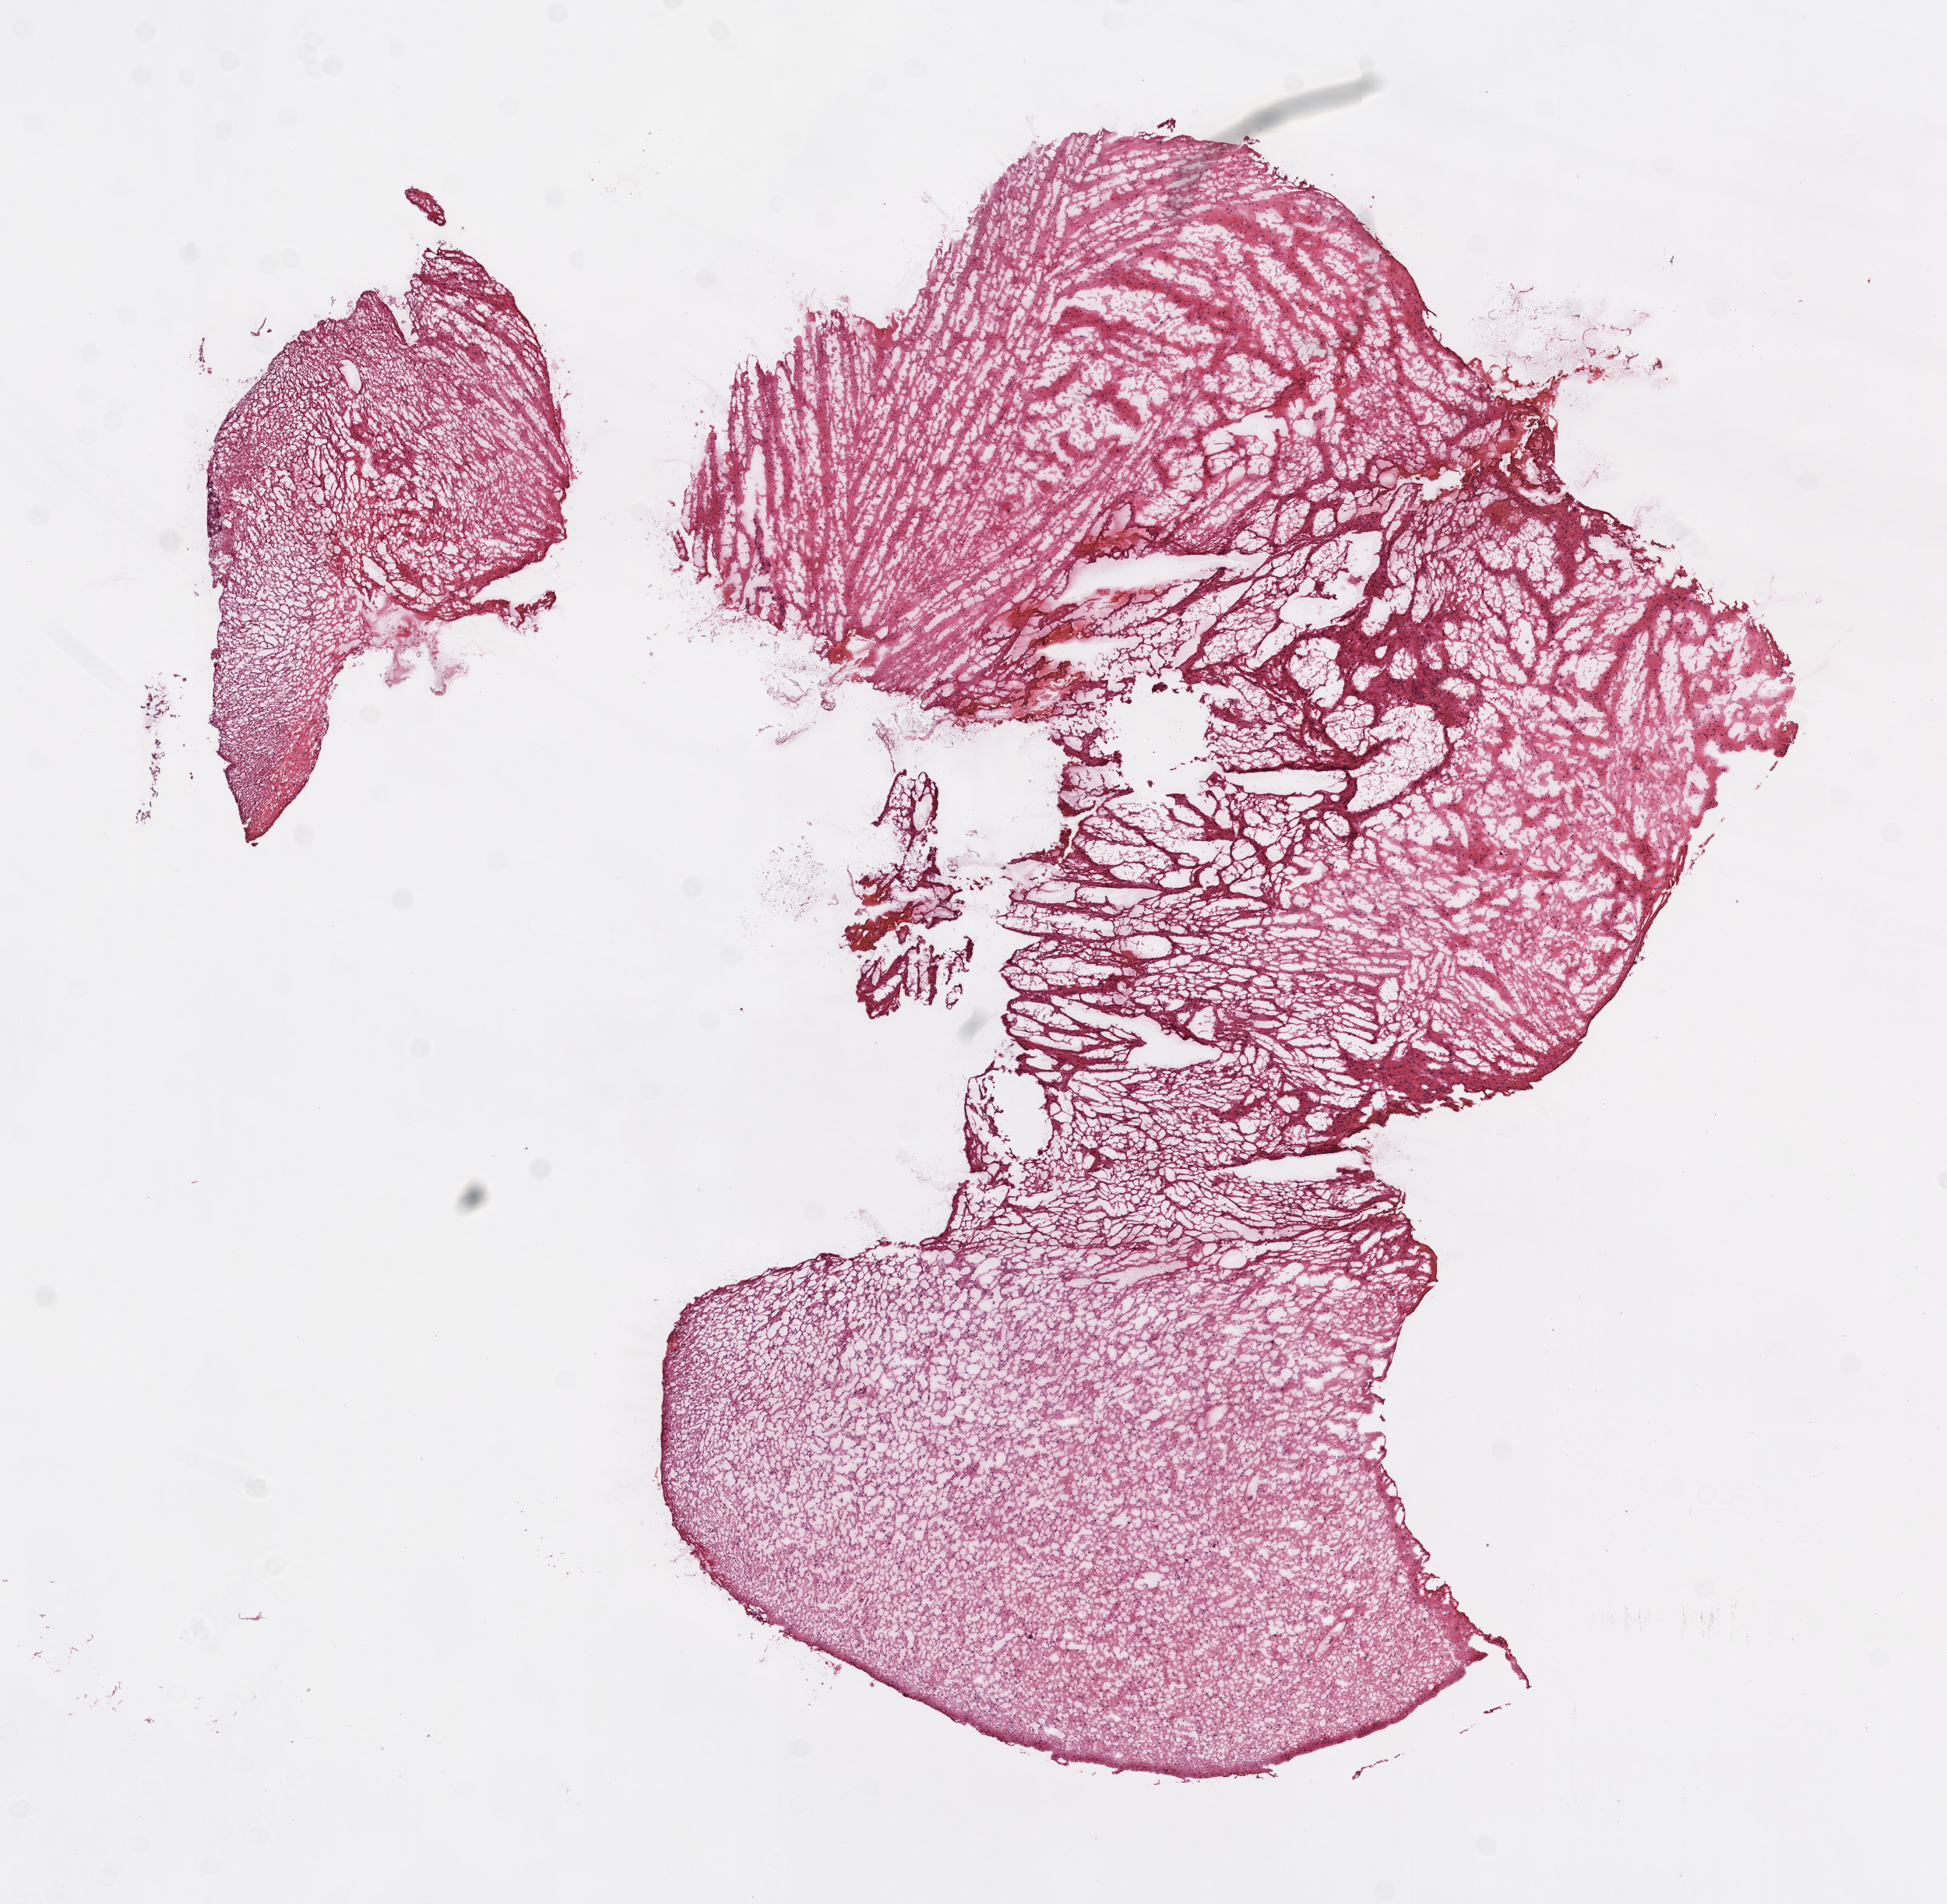
Whole-slide histology image, H&E-stained — a low-resolution overview of the entire scanned area, about 10.0 x 9.8 mm. Frozen section from the top of the tissue portion. Brain, primary tumour sample. Patient: male, age at initial diagnosis 50 years. Histologic grade: G2 (moderately differentiated). Pathologist review of this section (percent, as recorded): tumour cells 100%, tumour nuclei 60%, normal cells 0%, stromal cells 0%, necrosis 0%.
- histologic diagnosis: Astrocytoma, NOS